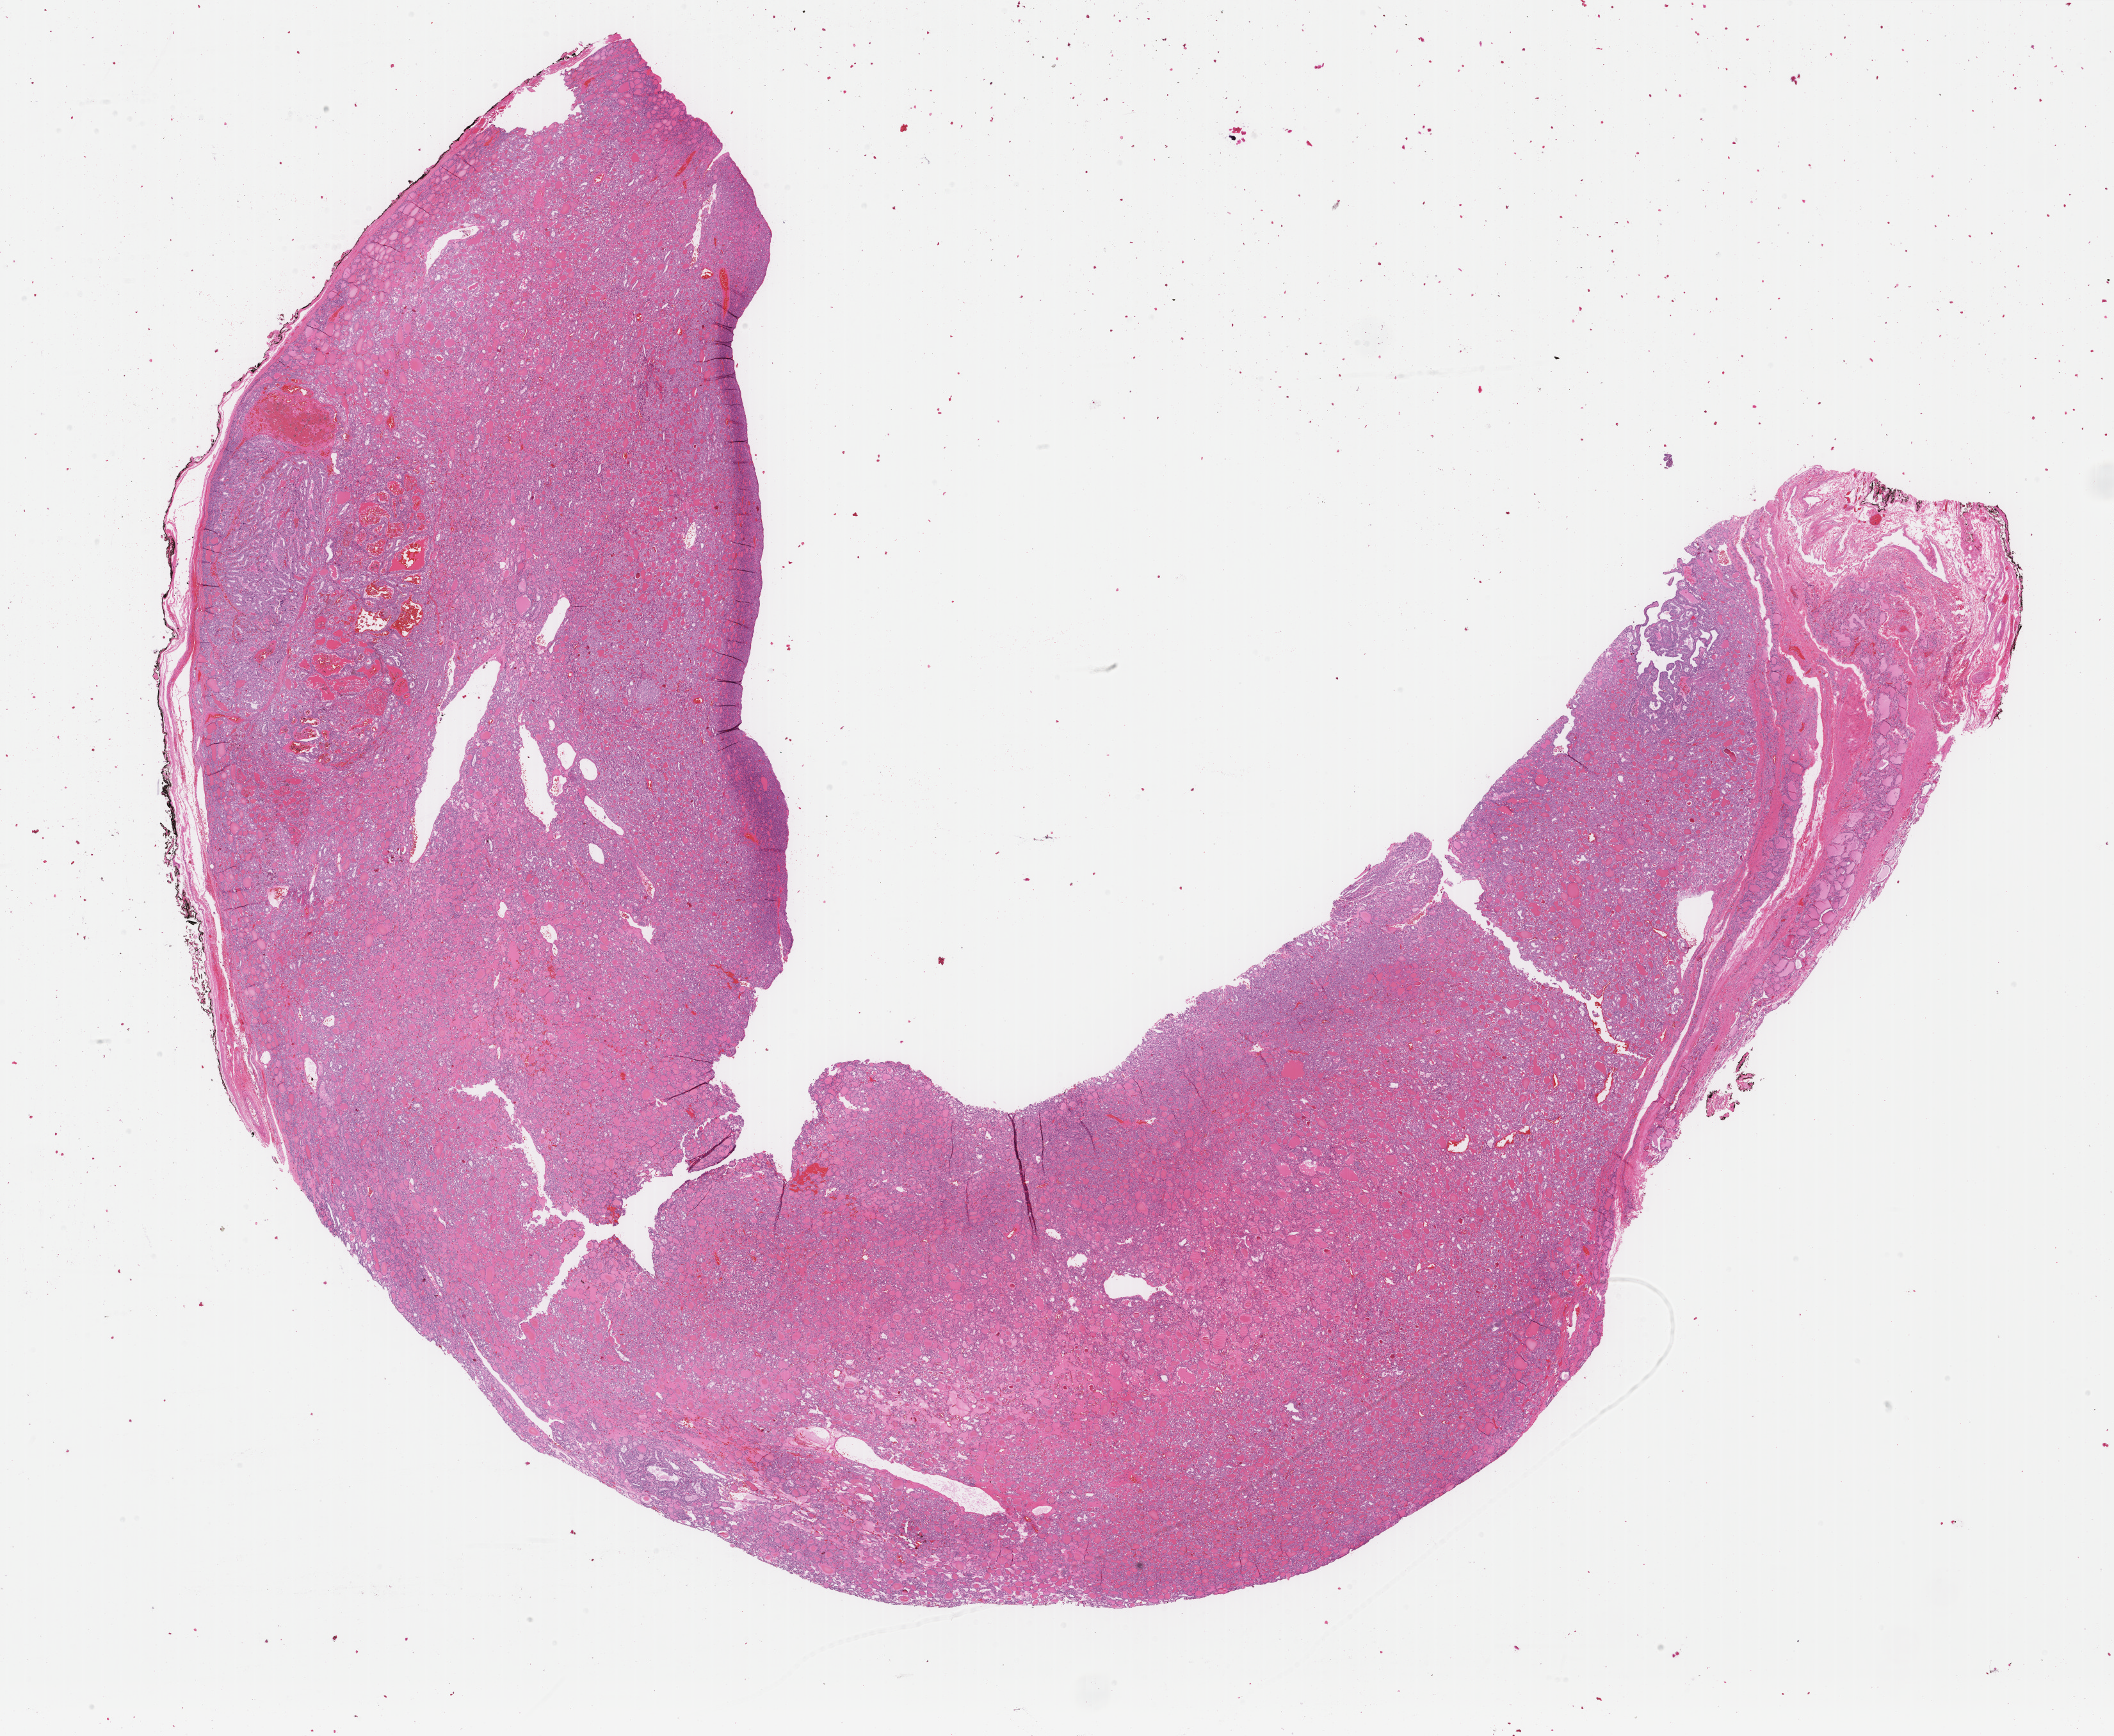
Hematoxylin and eosin (H&E) stained whole-slide image — low-resolution overview of the scanned area, about 26.2 x 21.5 mm (acquisition: 40x scan), formalin-fixed paraffin-embedded (FFPE) diagnostic section, primary tumour sample from the thyroid. Patient: female, age at initial diagnosis 20 years.
Diagnosis: Papillary adenocarcinoma, NOS. Lymph nodes positive (case pathology): 0 of 4 examined. TNM: T3 N0 MX. AJCC pathologic stage: I (6th edition). Laterality: left.